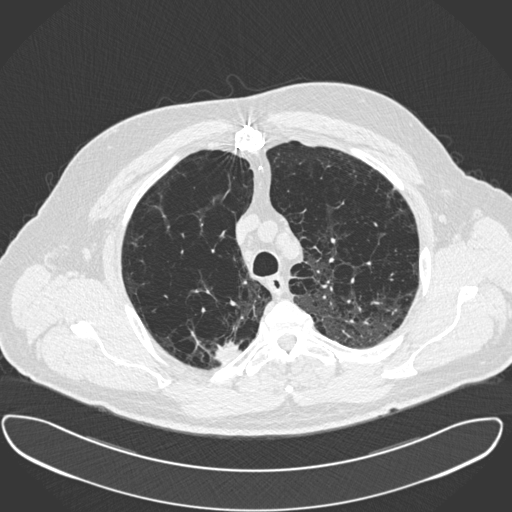
Low-dose screening chest CT, one axial slice; position 304 of 385 along the scan axis; reconstruction kernel B30f; 120 kVp; lung window (W 1500 / L -600 HU); 1 mm slice thickness; 512 × 512 image matrix, field of view 408 × 408 mm.
Annotated regions visible in this slice (manually delineated by an expert):
- lesion 1 (tumor, upper lobe of right lung): bounding box <214,339,240,363> (left, top, right, bottom; pixels)